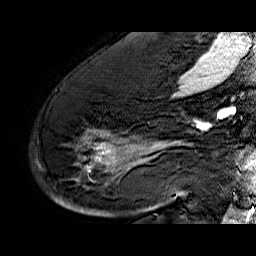
Breast MRI (dynamic contrast-enhanced), one sagittal slice. Position 38 of 60 along the scan axis. Dynamic contrast-enhanced series, time point 2 of 6 at this slice position (early post-contrast). 1.5 T. TE 6.4 ms, TR 32.9 ms. 4 mm slice thickness. 256 × 256 image matrix, field of view 200 × 200 mm. Female patient. From the clinical record (not read from this slice): setting: breast cancer imaged before/during neoadjuvant chemotherapy; receptor status: HR-positive, HER2-negative.
Annotated regions visible in this slice (semi-automatically segmented with operator editing):
- analysis volume of interest (the breast-tissue region the enhancement analysis was run in; not a lesion): bounding box (x1, y1, x2, y2) in pixels: (50, 74, 176, 210)
- tumour enhancement mask (voxels above the 100 % enhancement threshold inside the analysis volume of interest): (56, 130, 176, 202)